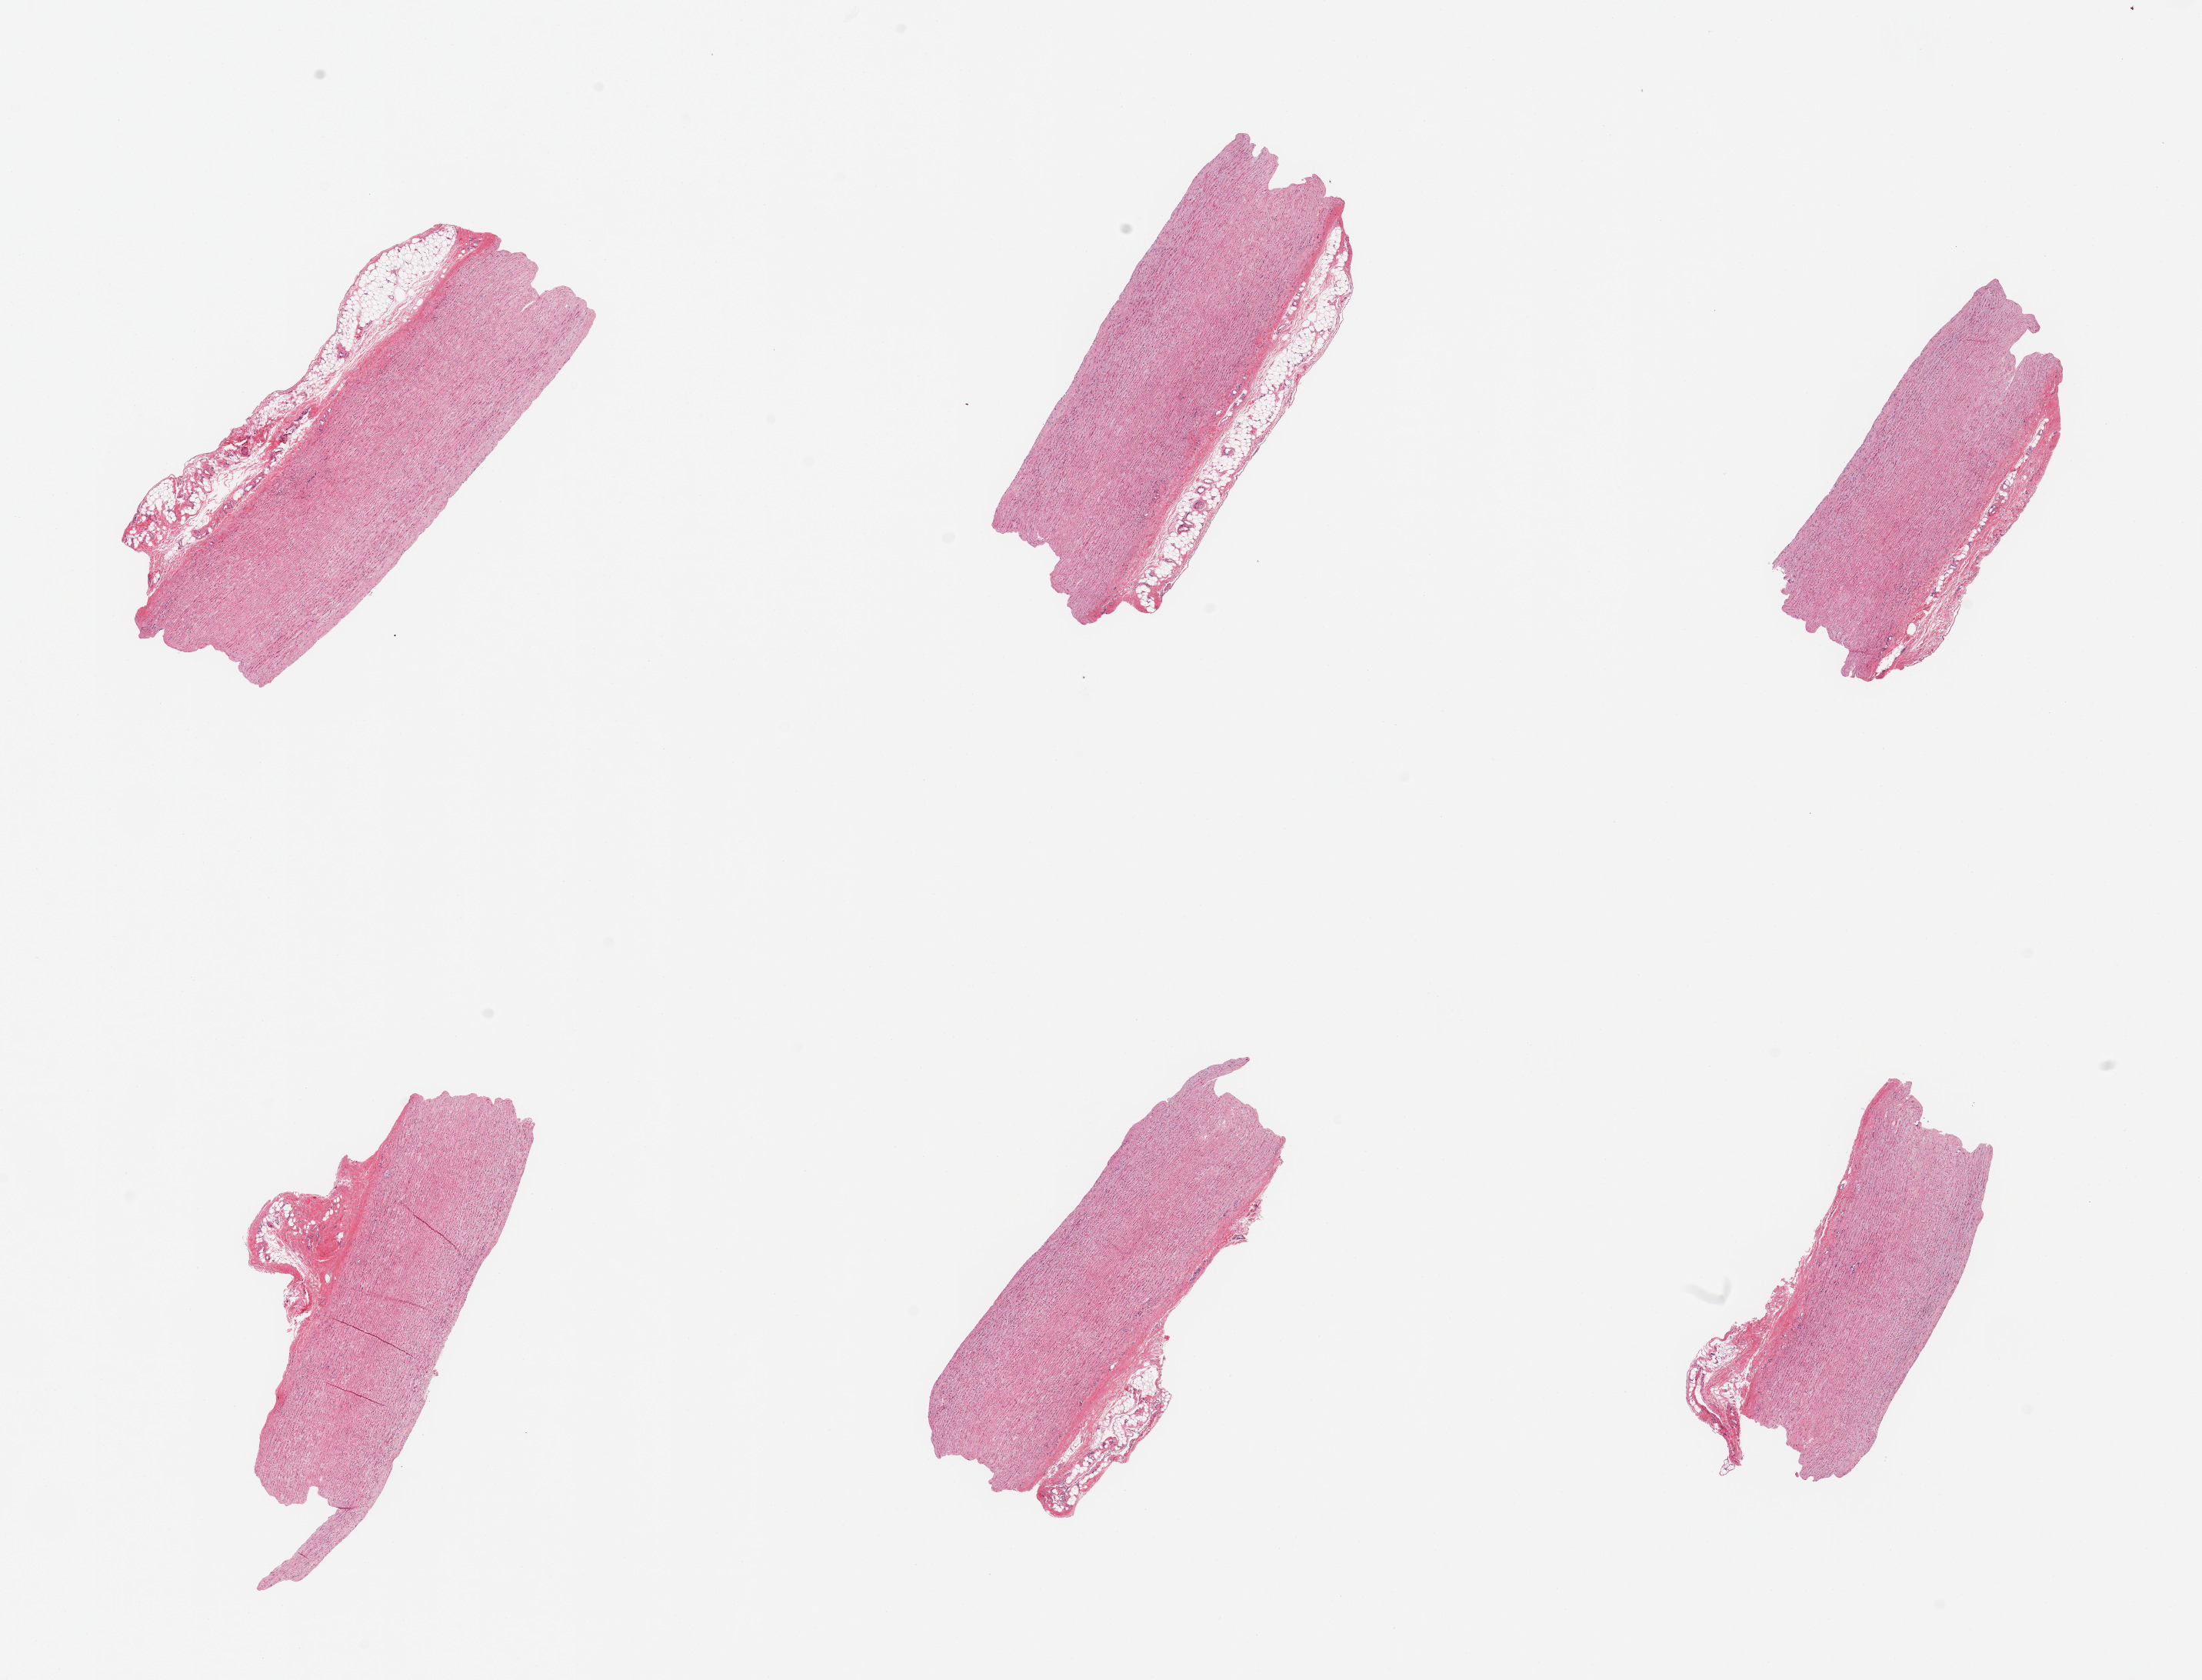
H&E whole-slide image, brightfield — whole scanned area (about 22.6 x 17.3 mm, acquisition: 20x scan) shown as a low-resolution overview. PAXgene-fixed, paraffin-embedded tissue. Sampled site (target tissue): aorta. Donor tissue sample. Donor sex: female.
Review note (as recorded): 6 pieces; several include residual attached fat.